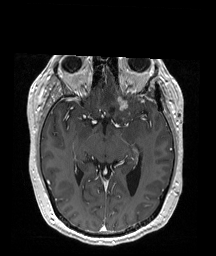
Brain MRI from a brain-tumour surgery series, one axial slice. Slice 108 of 192 in the series (ordered by position). T1-weighted post-contrast. 1 mm slice thickness. 216 × 256 image matrix. From the clinical record (not read from this slice): histopathology: Oligodendroglioma; WHO grade: 2; IDH mutation: yes; tumour location: Left Frontal (septal).
Outlined on this slice (expert manual segmentation):
- tumour: box from (x=107, y=95) to (x=132, y=108) px